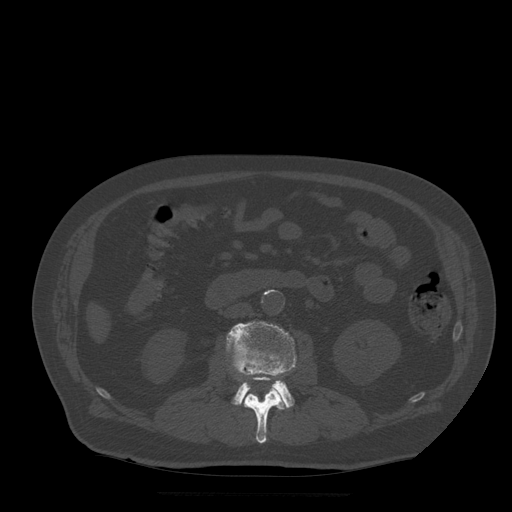
CT including the spine, one axial slice. Slice 156 of 522 in the series (ordered by position). Bone window (W 1800 / L 400 HU). 1.25 mm slice thickness. 512 × 512 image matrix, field of view 420 × 420 mm. Patient age 72 years. Case-level facts recorded for this patient, not image findings: primary cancer: prostate.
Structures marked on this image (semi-automatically segmented with operator editing):
- L2 vertebra: box from (x=244, y=374) to (x=286, y=444) px
- L3 vertebra: (x=227, y=321)–(x=297, y=409)